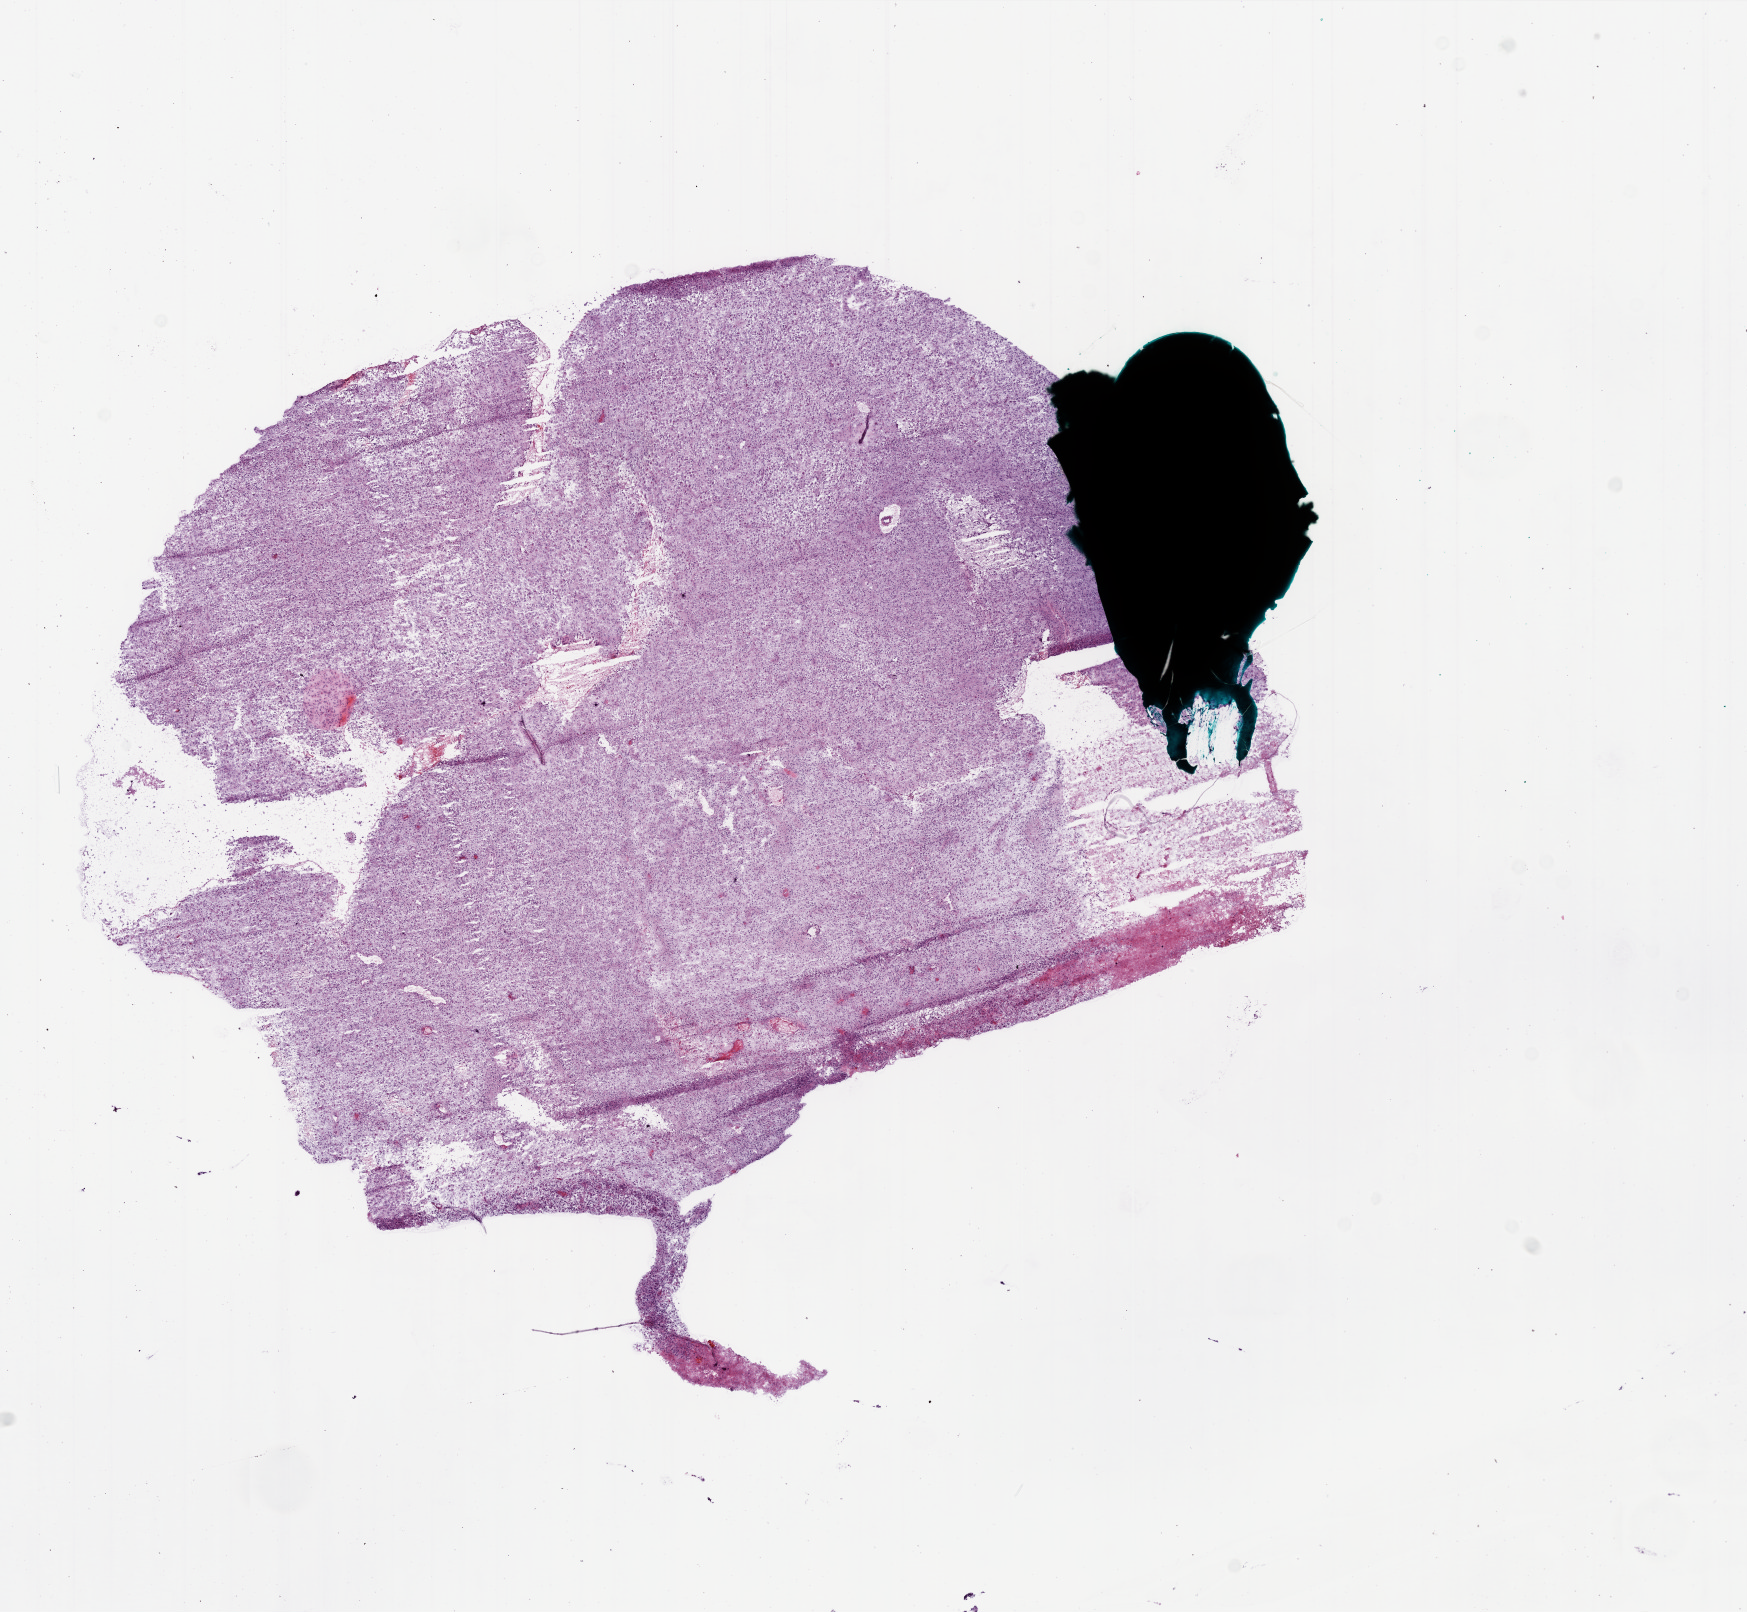
Digitized H&E-stained tissue section (whole slide), low-resolution overview of the scanned area, about 14.0 x 12.9 mm (acquisition: 20x scan); frozen section from the bottom of the tissue portion; primary tumour sample from the brain. Male patient; age at initial diagnosis 52 years. Slide review estimates, as recorded: tumour cells 90%, tumour nuclei 95%, normal cells 0%, stromal cells 0%, necrosis 10%.
Histologic diagnosis: Glioblastoma.